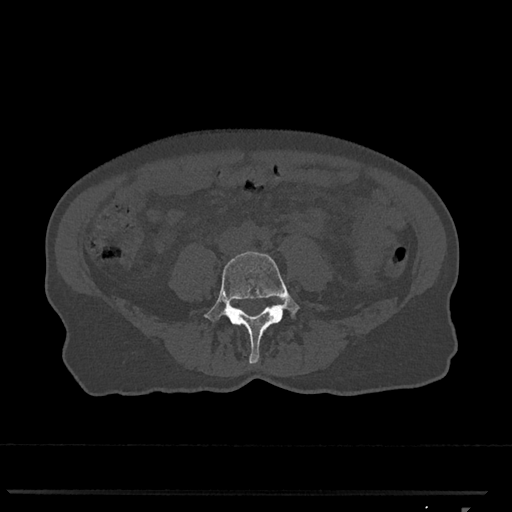
CT including the spine, one axial slice; slice 208 of 793 in the series (ordered by position); reconstruction kernel Br40s/3; bone window (W 1800 / L 400 HU); 512 × 512 image matrix. Patient: female, 62 years. Case-level facts recorded for this patient, not image findings: primary cancer: renal.
Annotated regions visible in this slice (semi-automatically segmented with operator editing):
- L4 vertebra: bounding box [x1, y1, x2, y2] px = [204, 251, 300, 364]